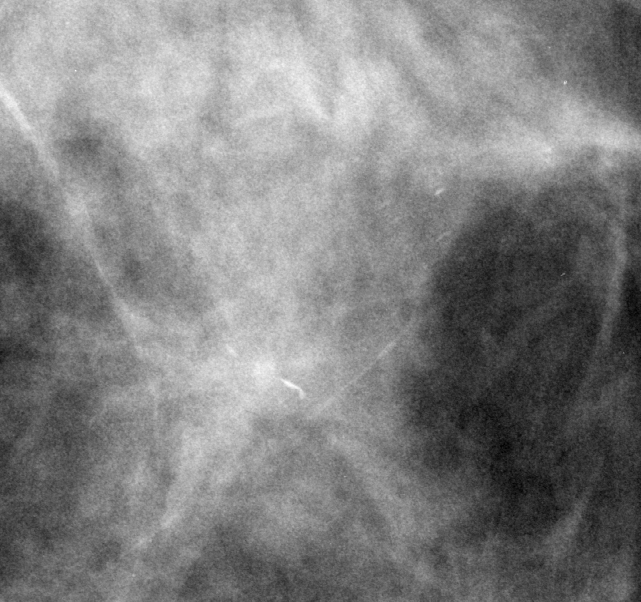
Crop from a digitized film mammogram around one marked abnormality; left breast; CC view.
- Finding: calcifications, morphology fine linear branching, distribution linear; BI-RADS assessment category 4; pathology (as recorded): benign.